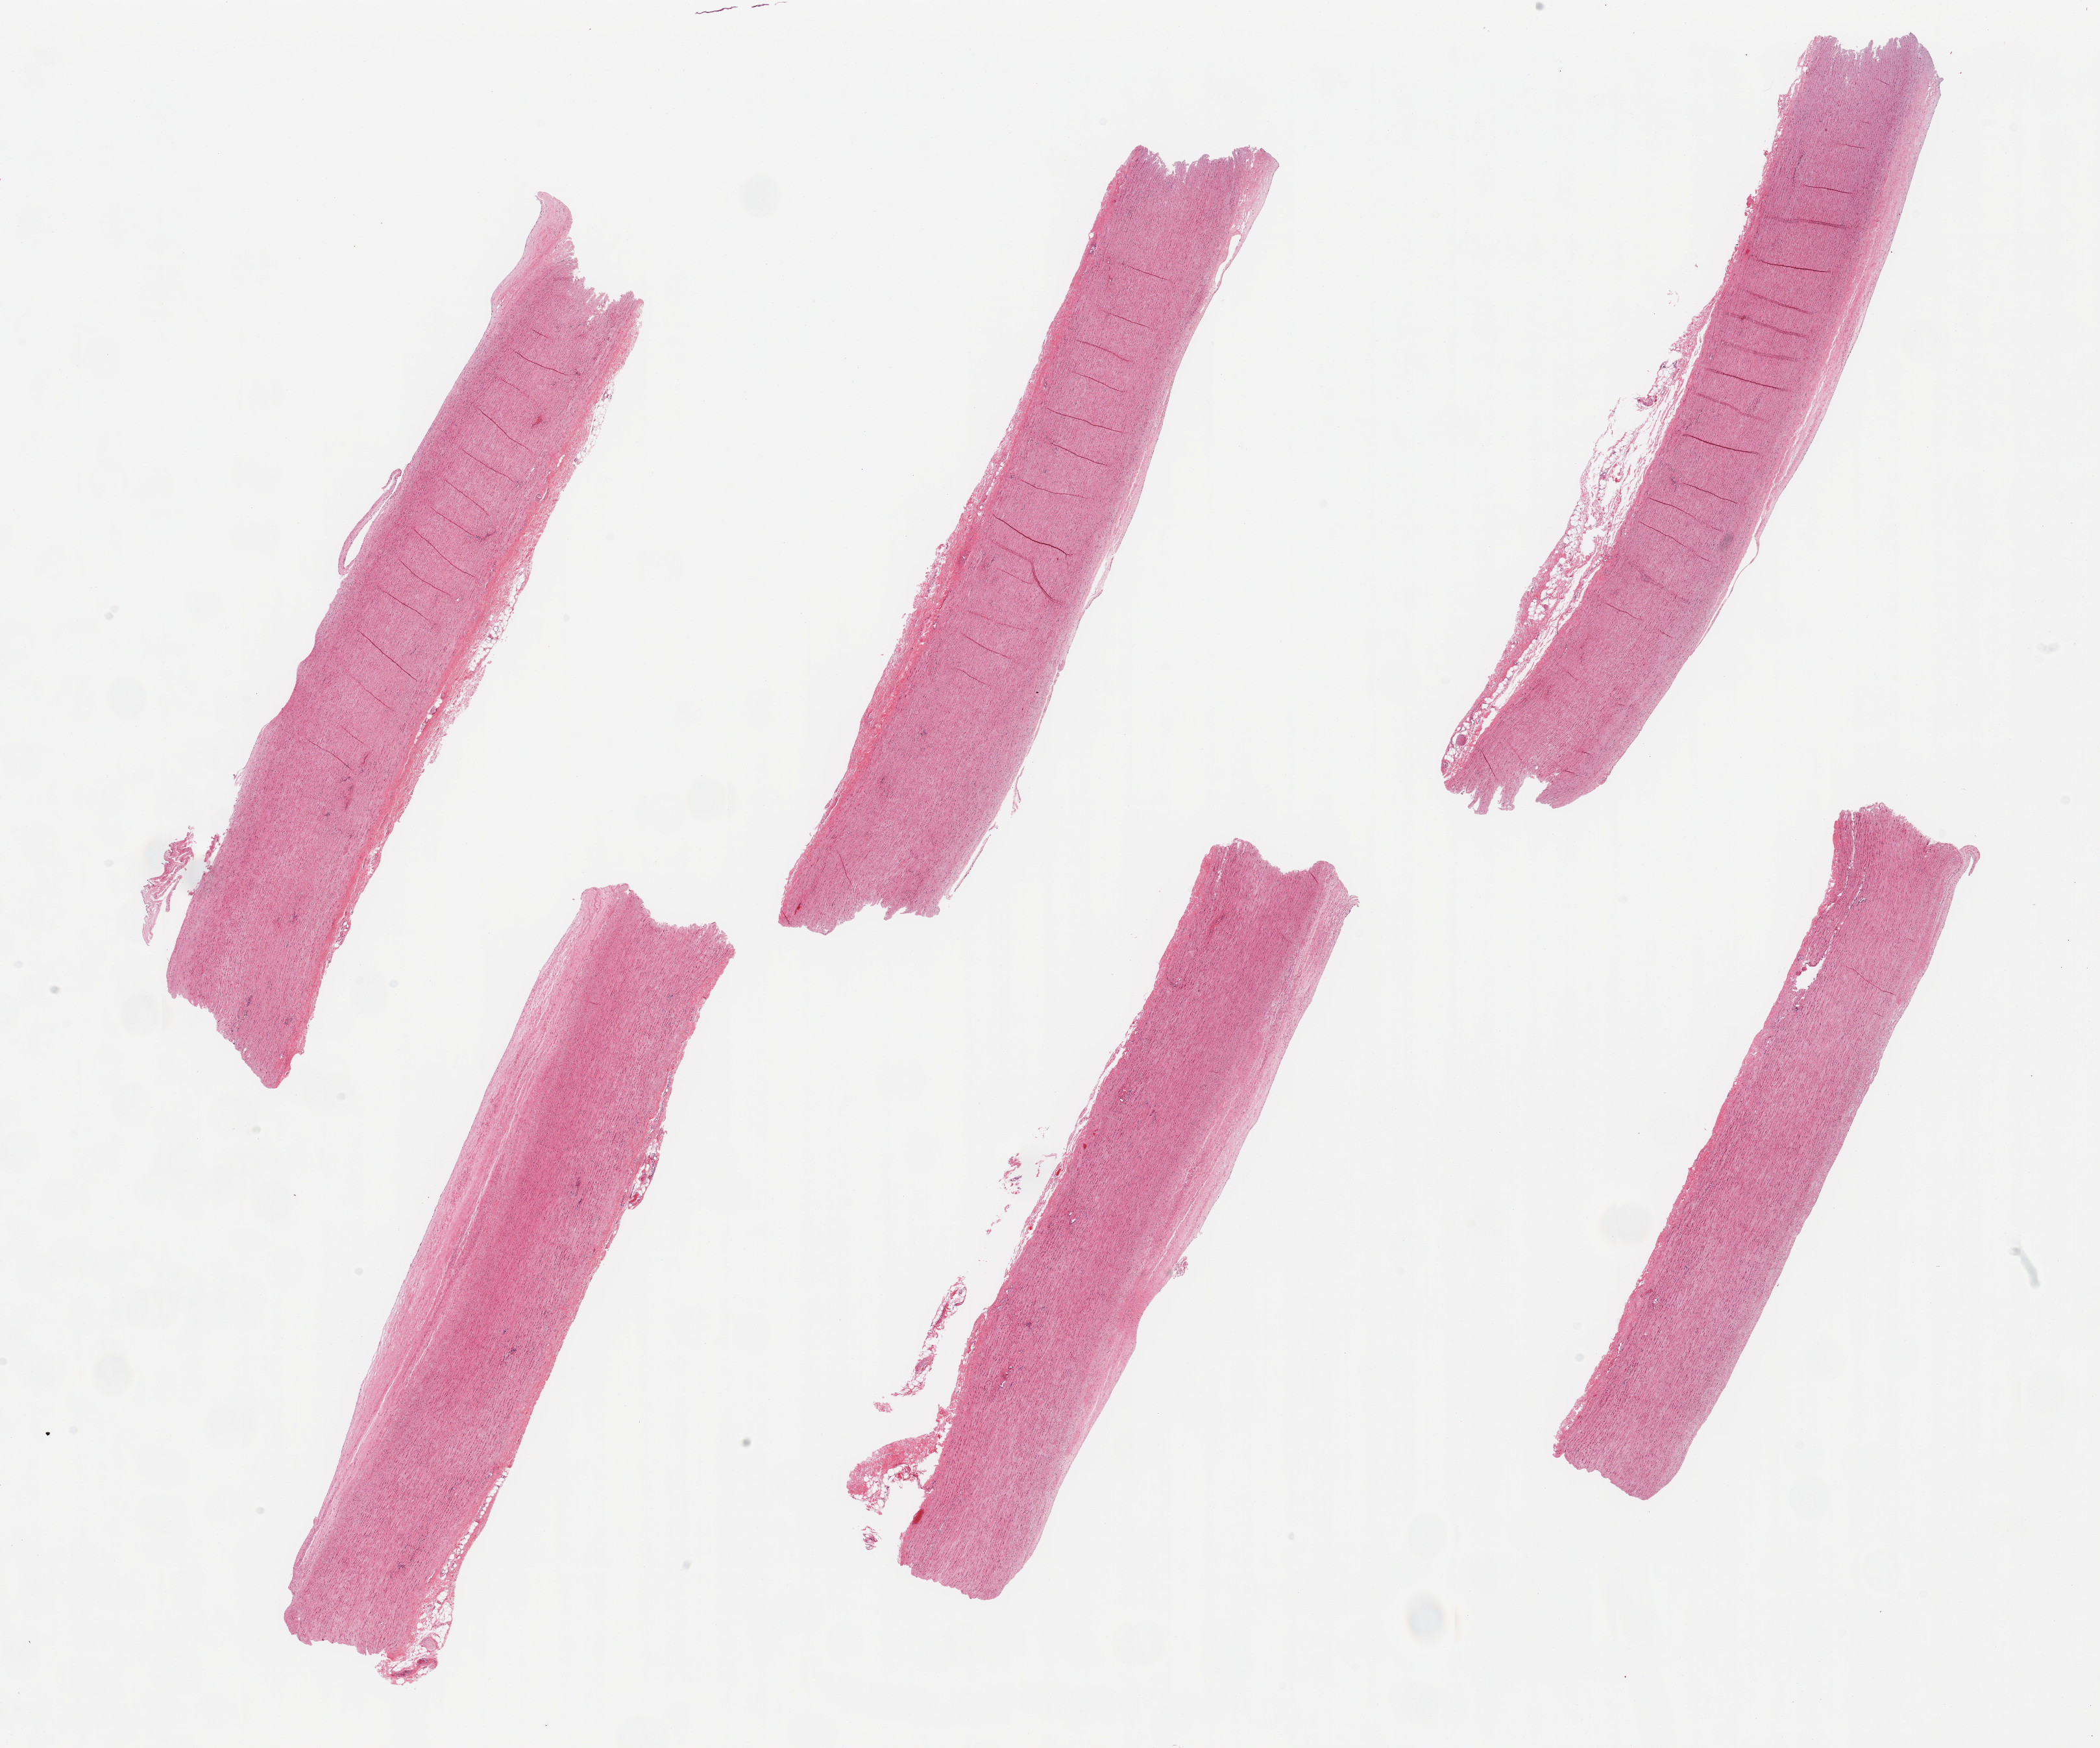
H&E whole-slide image, whole scanned area (about 25.6 x 21.3 mm, slide scanned at 20x) shown as a low-resolution overview. PAXgene-fixed, paraffin-embedded tissue. Target tissue: aorta. Donor tissue sample. Donor sex: male.
Reviewer comment on this tissue sample: 6 pieces, atherosis up to ~0.3mm.